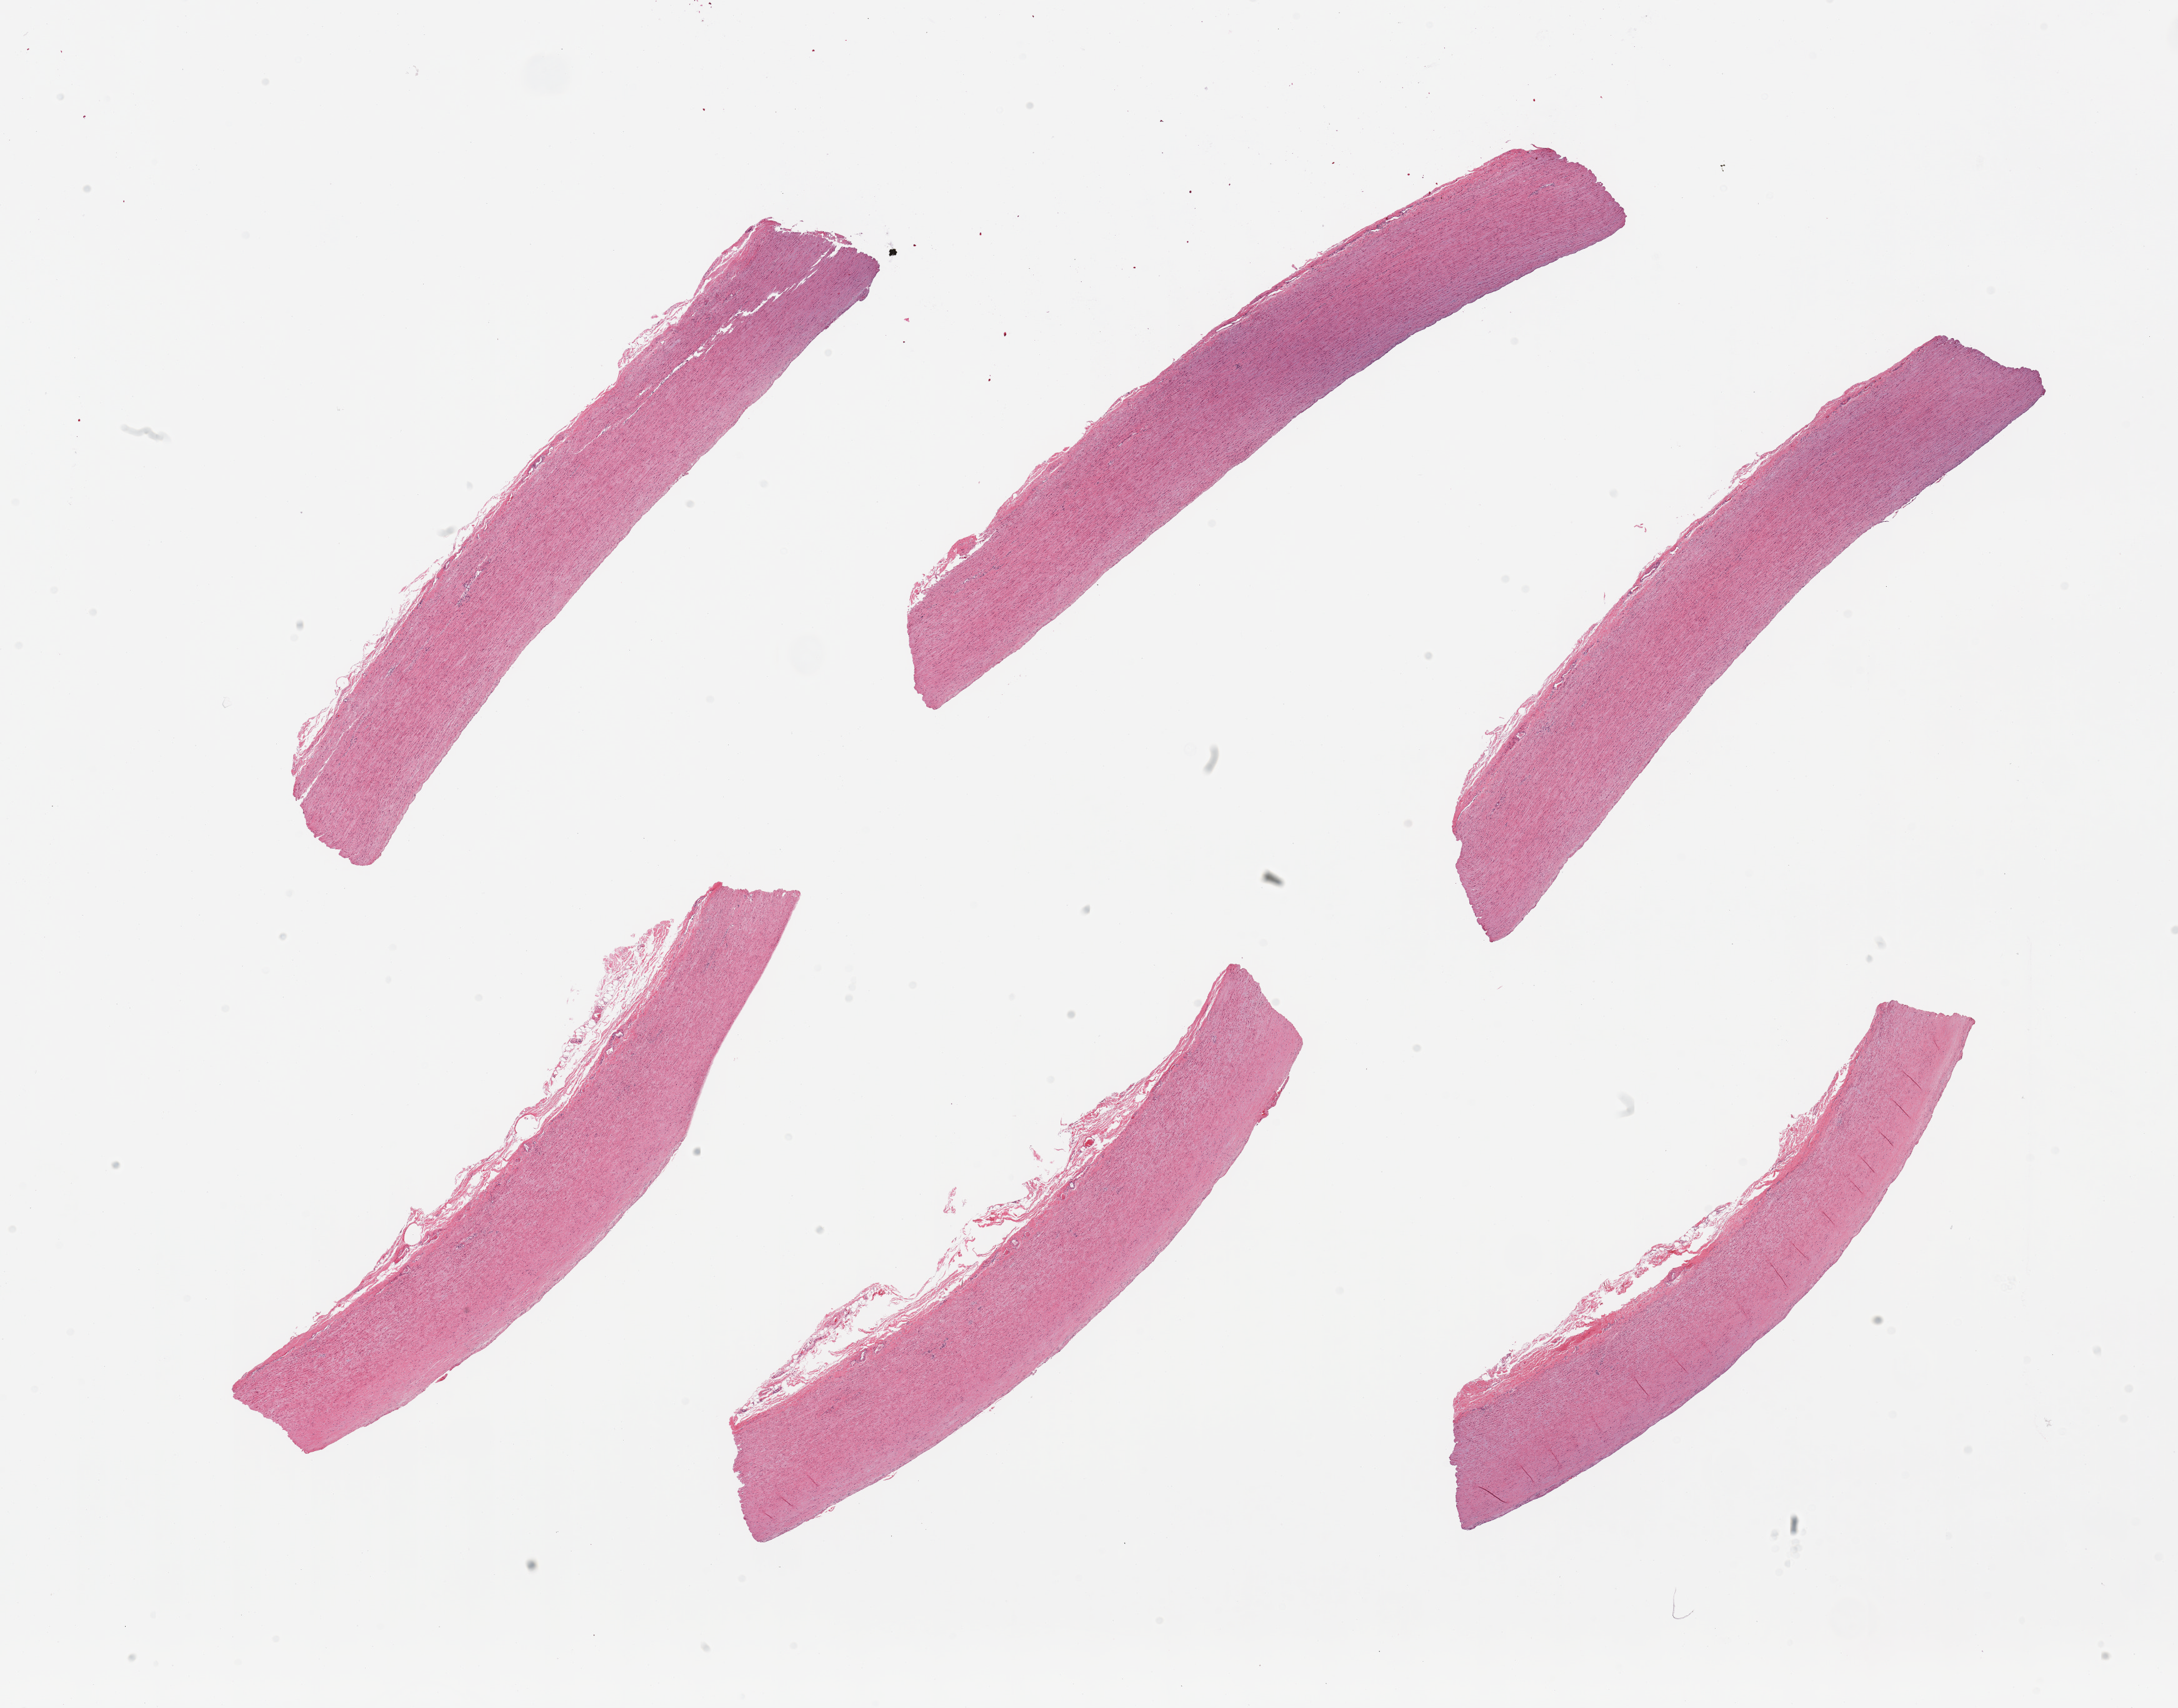
Whole-slide image, hematoxylin and eosin (H&E) stain, brightfield — low-resolution overview of the scanned area, about 27.6 x 21.6 mm (slide scanned at 20x); PAXgene-fixed, paraffin-embedded tissue; section of aorta (target tissue); donor tissue sample. Donor sex: male.
Reviewer comment on this tissue sample: 6 pieces, minimal atherosis.